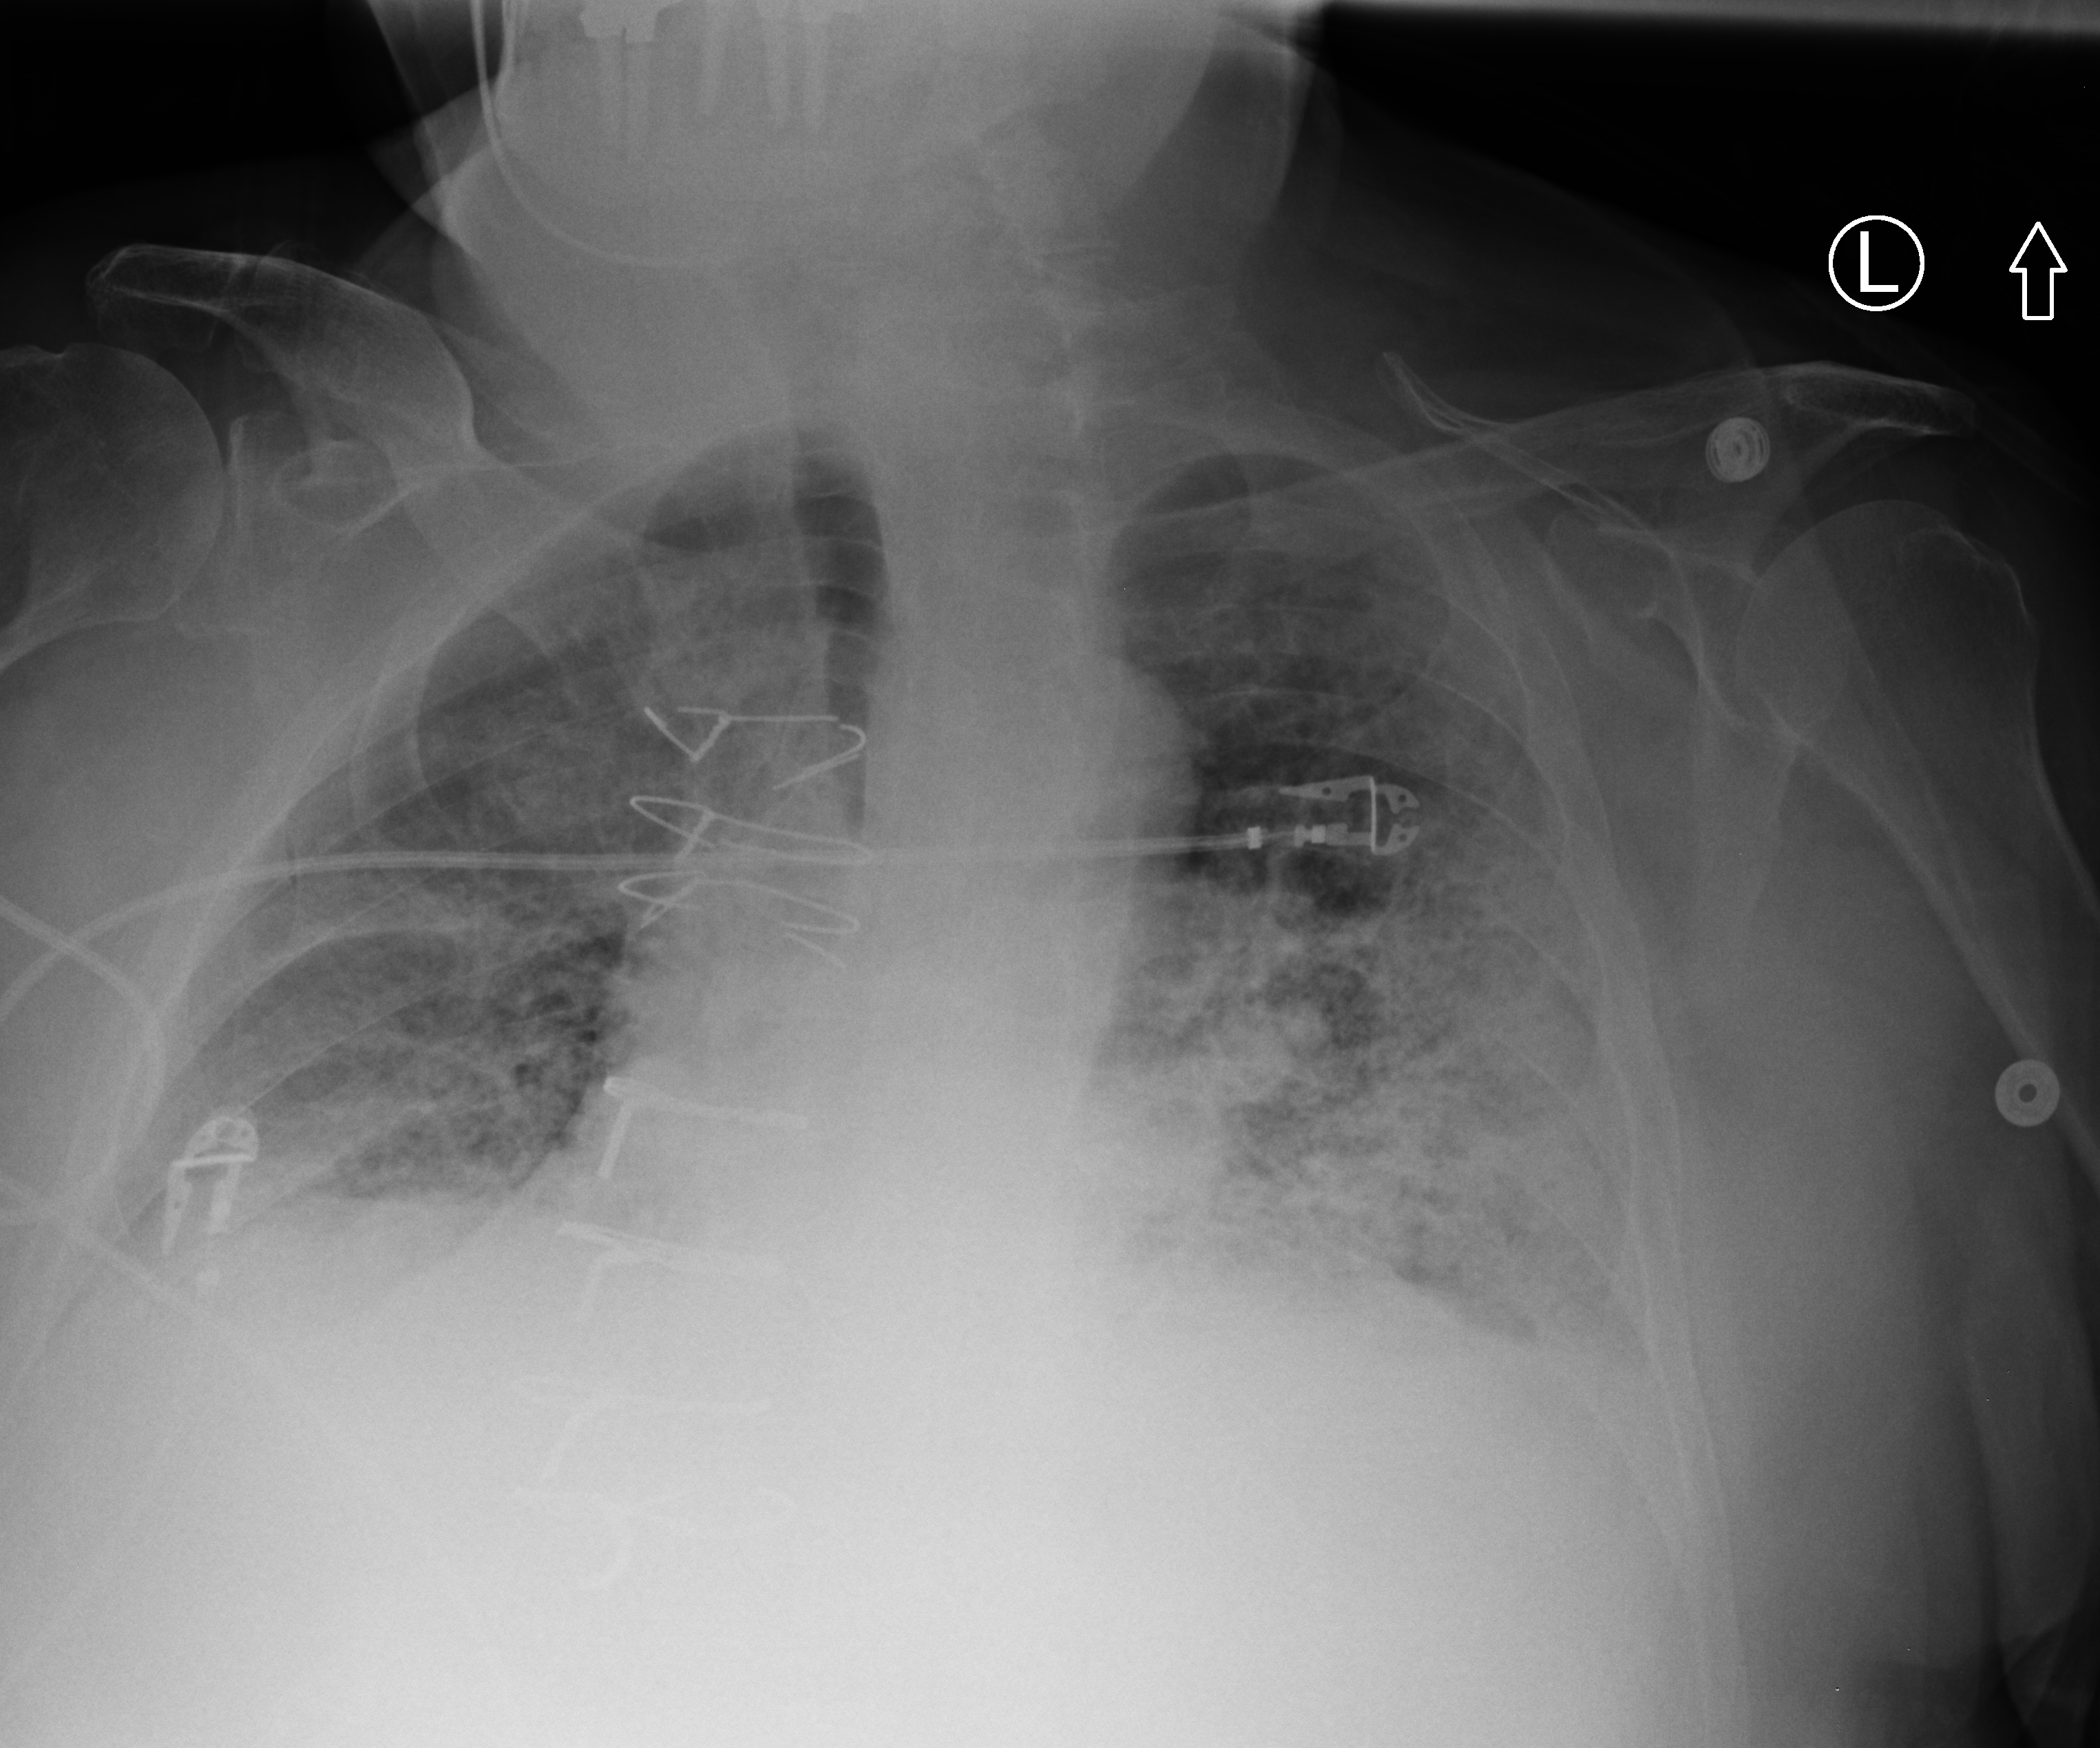
Bedside chest radiograph (computed radiography), anteroposterior (AP) projection. Patient hospitalised with COVID-19; male, aged 75–90 years.
Admission-level facts for this patient (not findings on this image; timing relative to this image not recorded):
- chronic kidney disease (admission record): yes